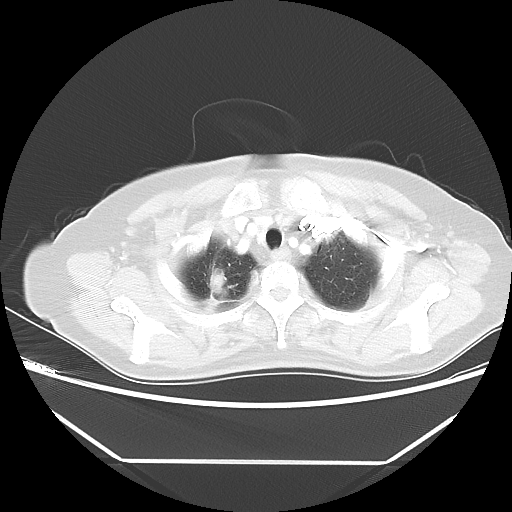
Chest CT, one axial slice; position 44 of 48 along the scan axis; reconstruction kernel LUNG; lung window (W 1500 / L -600 HU); 5 mm slice thickness; 512 × 512 image matrix, field of view 360 × 360 mm. Patient: female, 65 years. From the clinical record (not read from this slice): clinical TNM (as recorded): T1c N1 M1.
Annotated regions visible in this slice (bounding box drawn by a radiologist):
- lung tumour (recorded histology: adenocarcinoma): box from (x=207, y=265) to (x=235, y=302) px